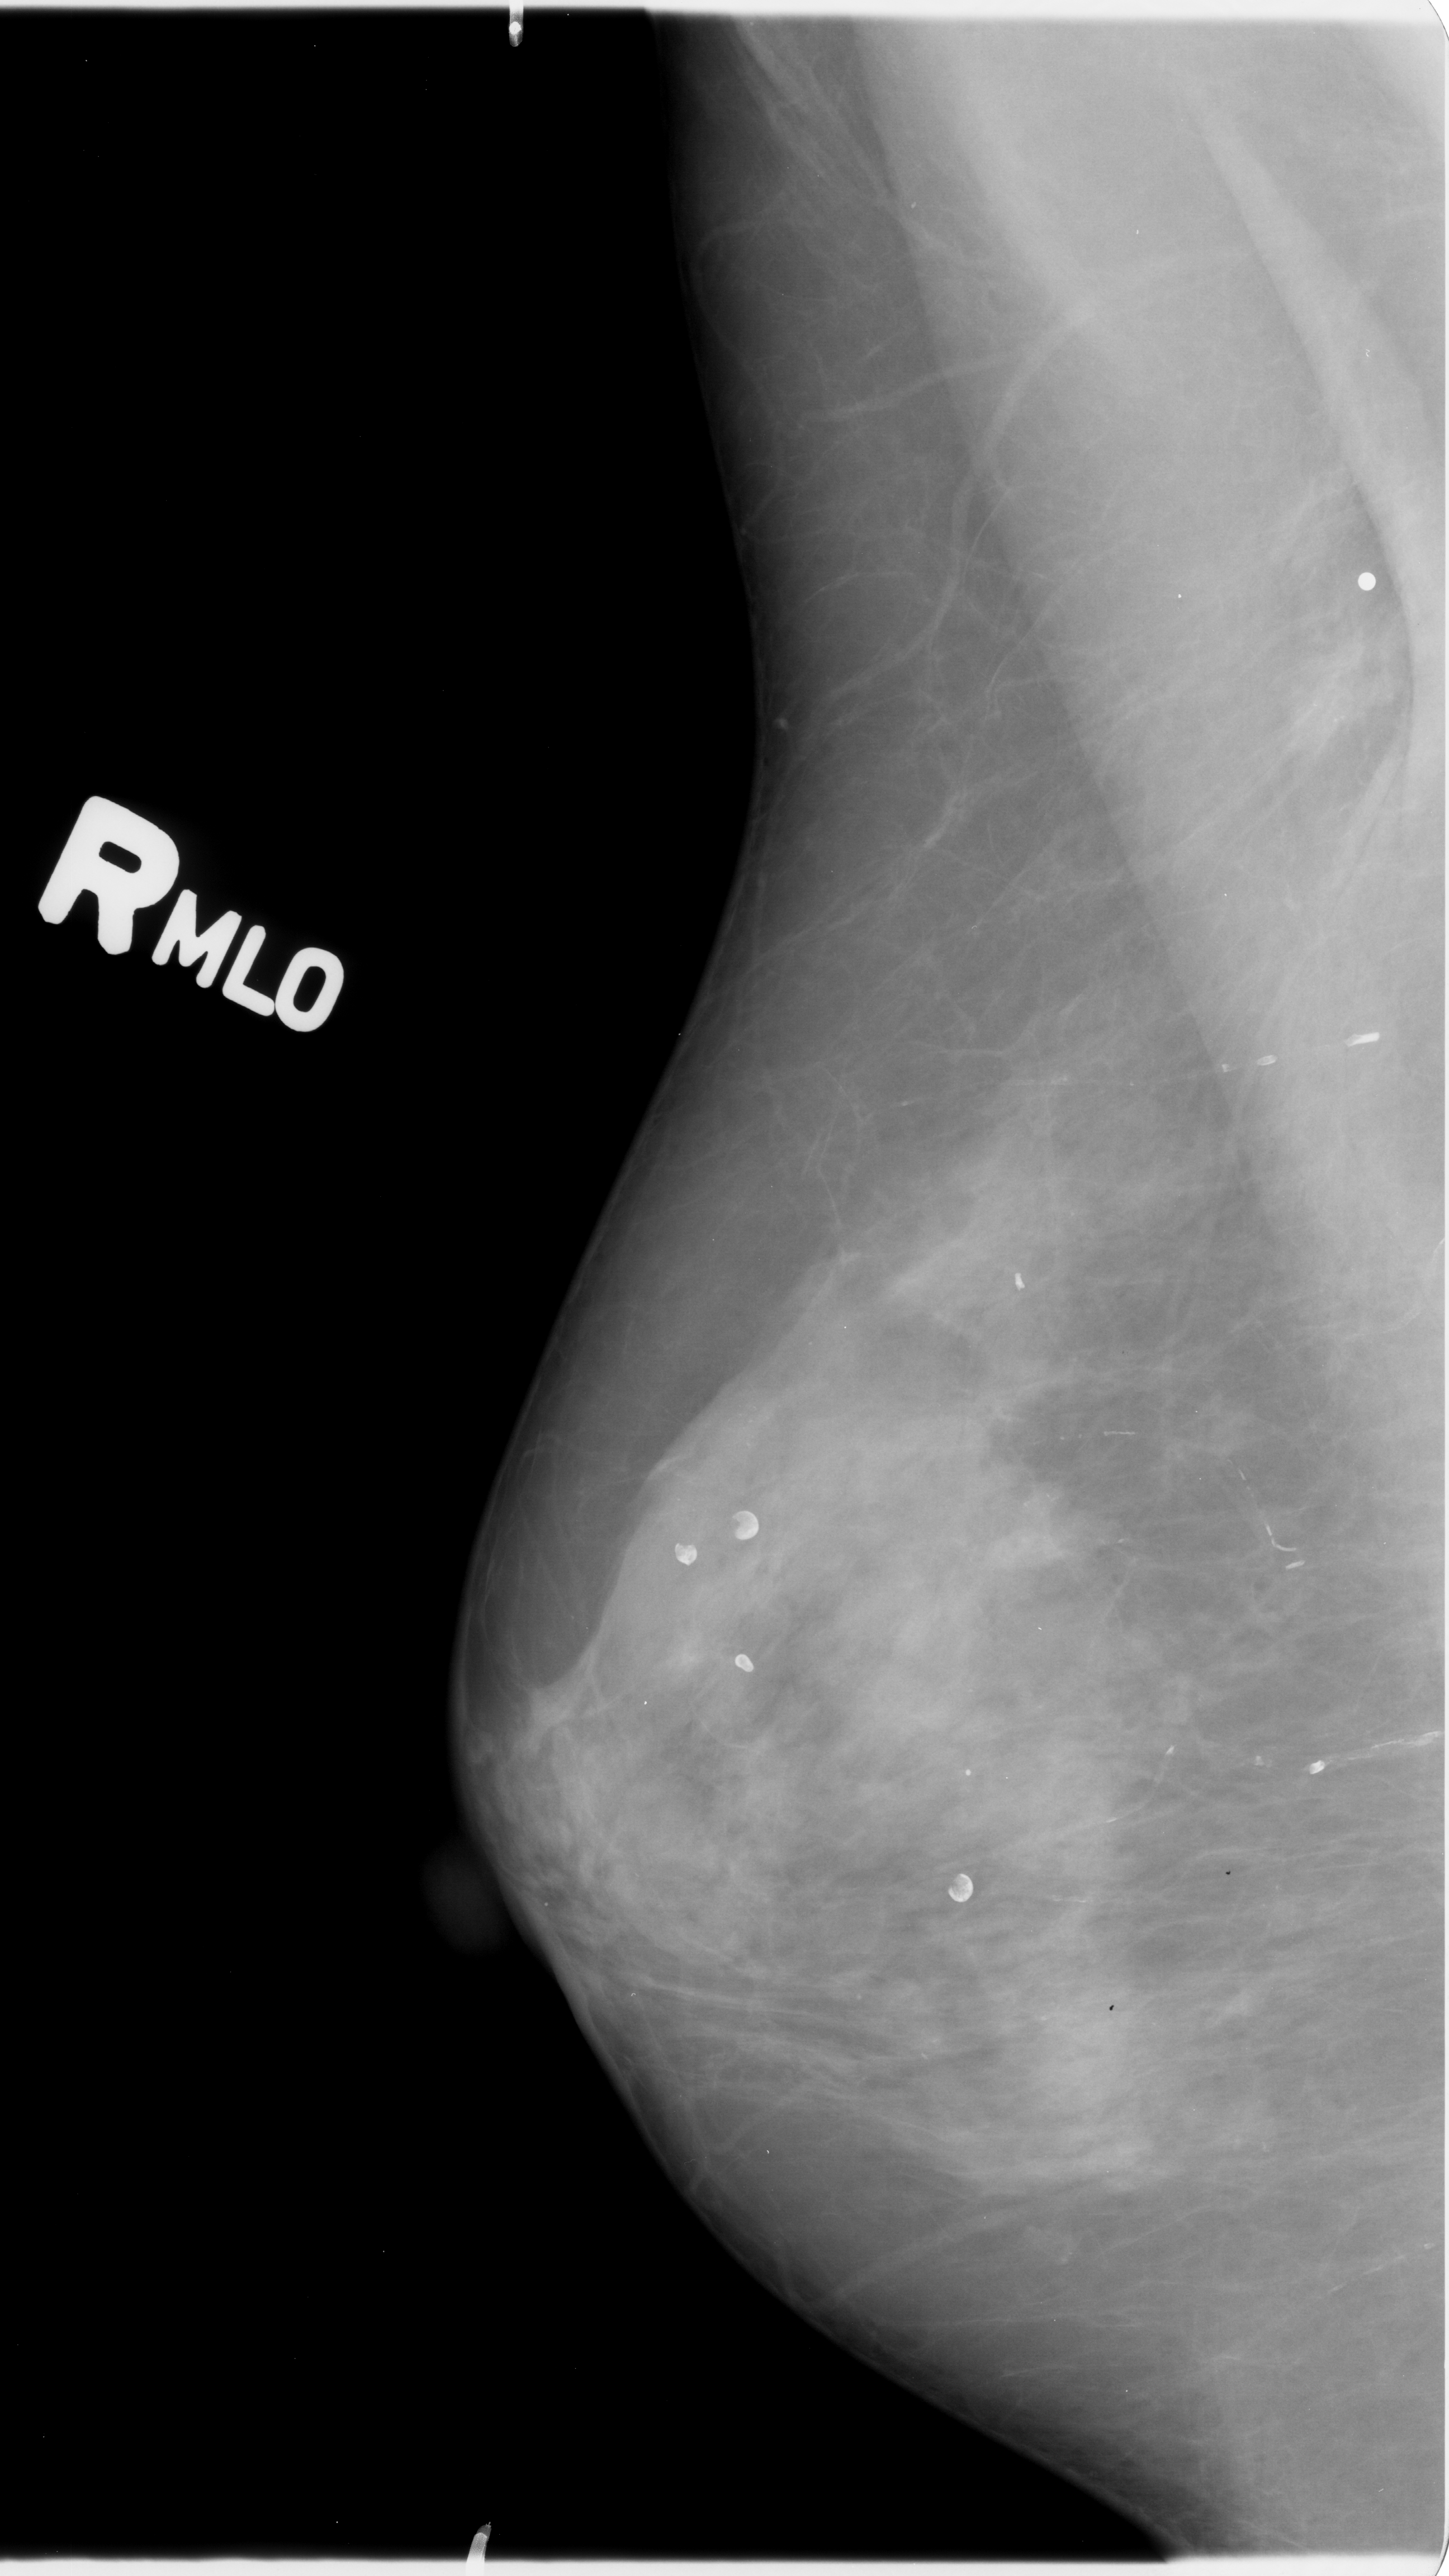
Mammogram (digitized film); right breast; MLO view; 1449 × 2576 image matrix.
Marked abnormalities (boxes around the expert regions of interest):
- mass, shape irregular, margins spiculated; BI-RADS assessment category 4; subtlety rating 3 on a 1 (subtle) to 5 (obvious) scale; pathology result (as recorded, not read from the image): malignant: box from (x=1276, y=633) to (x=1394, y=771) px